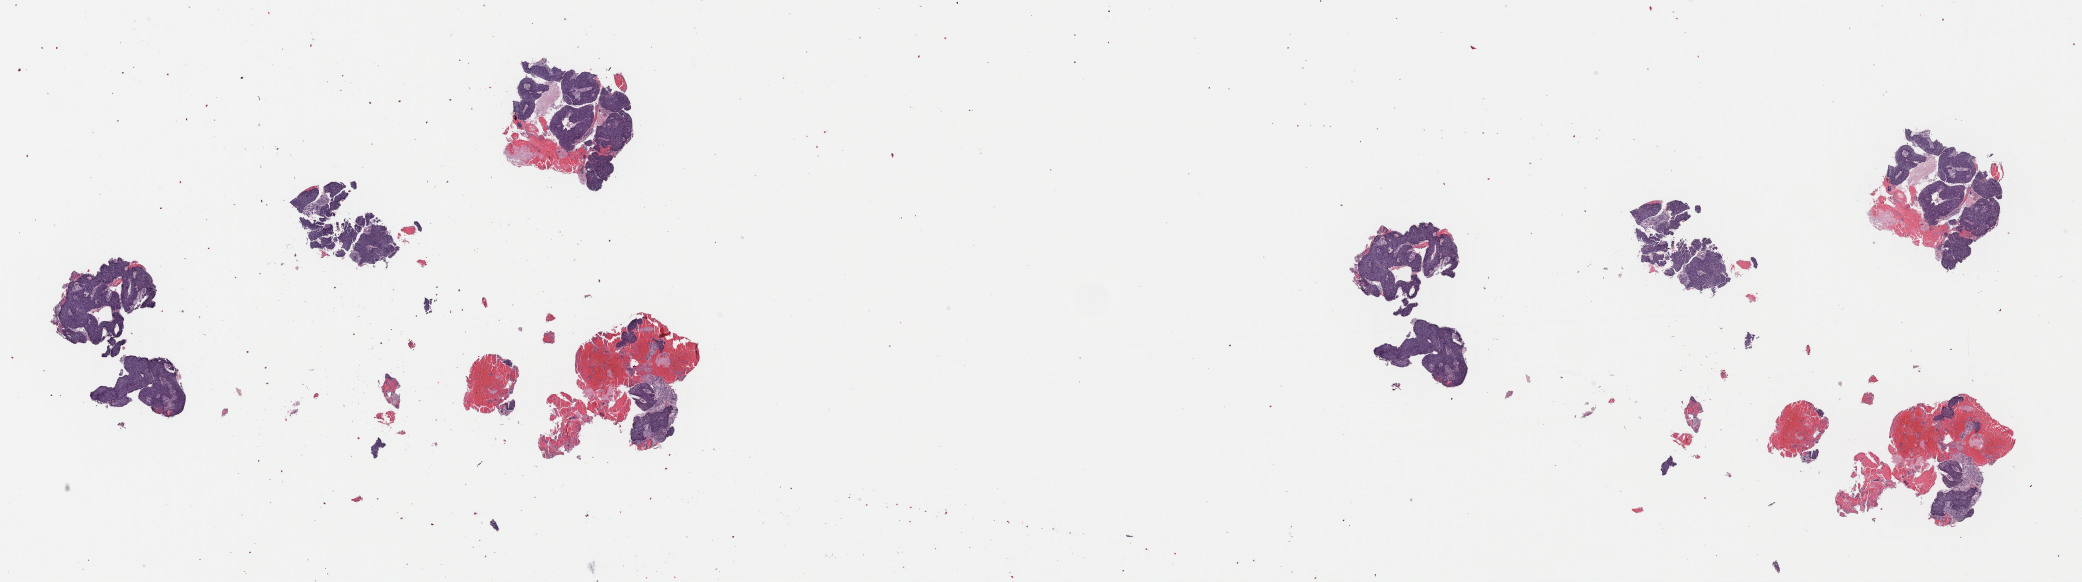
H&E whole-slide image, a low-resolution overview of the entire scanned area, about 32.9 x 9.2 mm; FFPE section; cervix, primary tumour sample. Patient: female, age at initial diagnosis 37 years.
Pathologic diagnosis: Squamous cell carcinoma, NOS (cervix uteri).